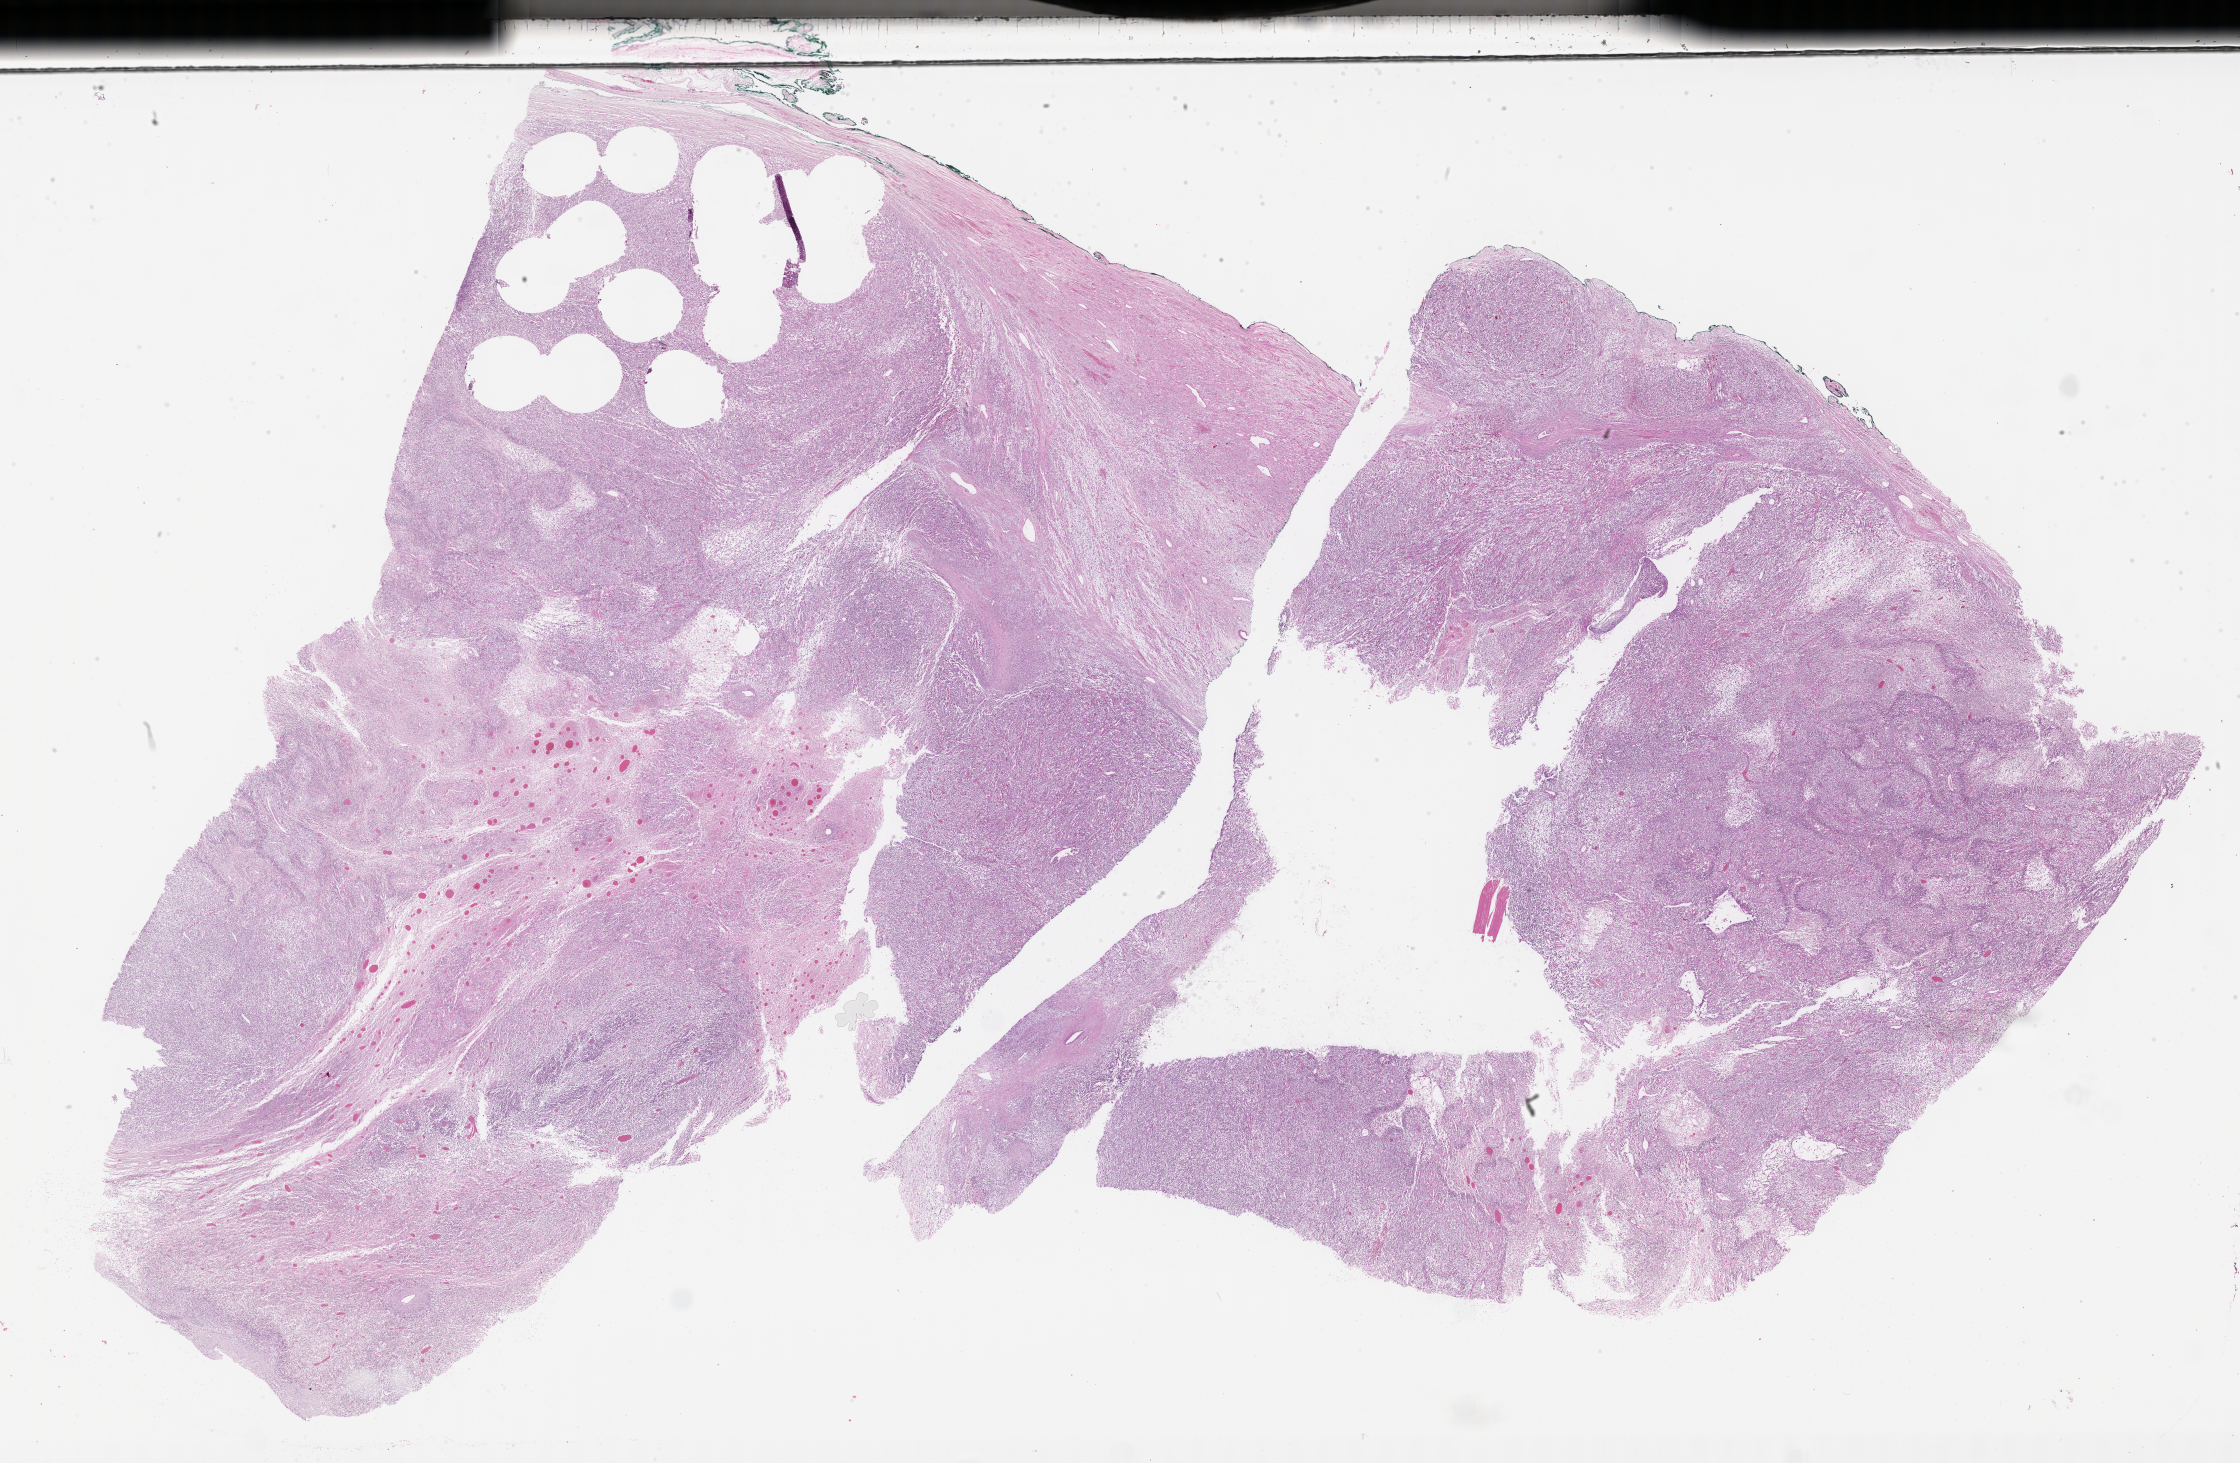
Whole-slide image, haematoxylin and eosin stain of tumor tissue, shown as a low-resolution overview of the whole scanned area (about 36.2 x 23.7 mm); formalin-fixed, paraffin-embedded (FFPE) tissue; site: scrotum, right. Patient: male, age 1.9 years at diagnosis.
• metastatic status at presentation (as recorded): non-metastatic
• stage (as recorded): 1
• diagnosis: rhabdomyosarcoma; histological classification: embryonal rhabdomyosarcoma